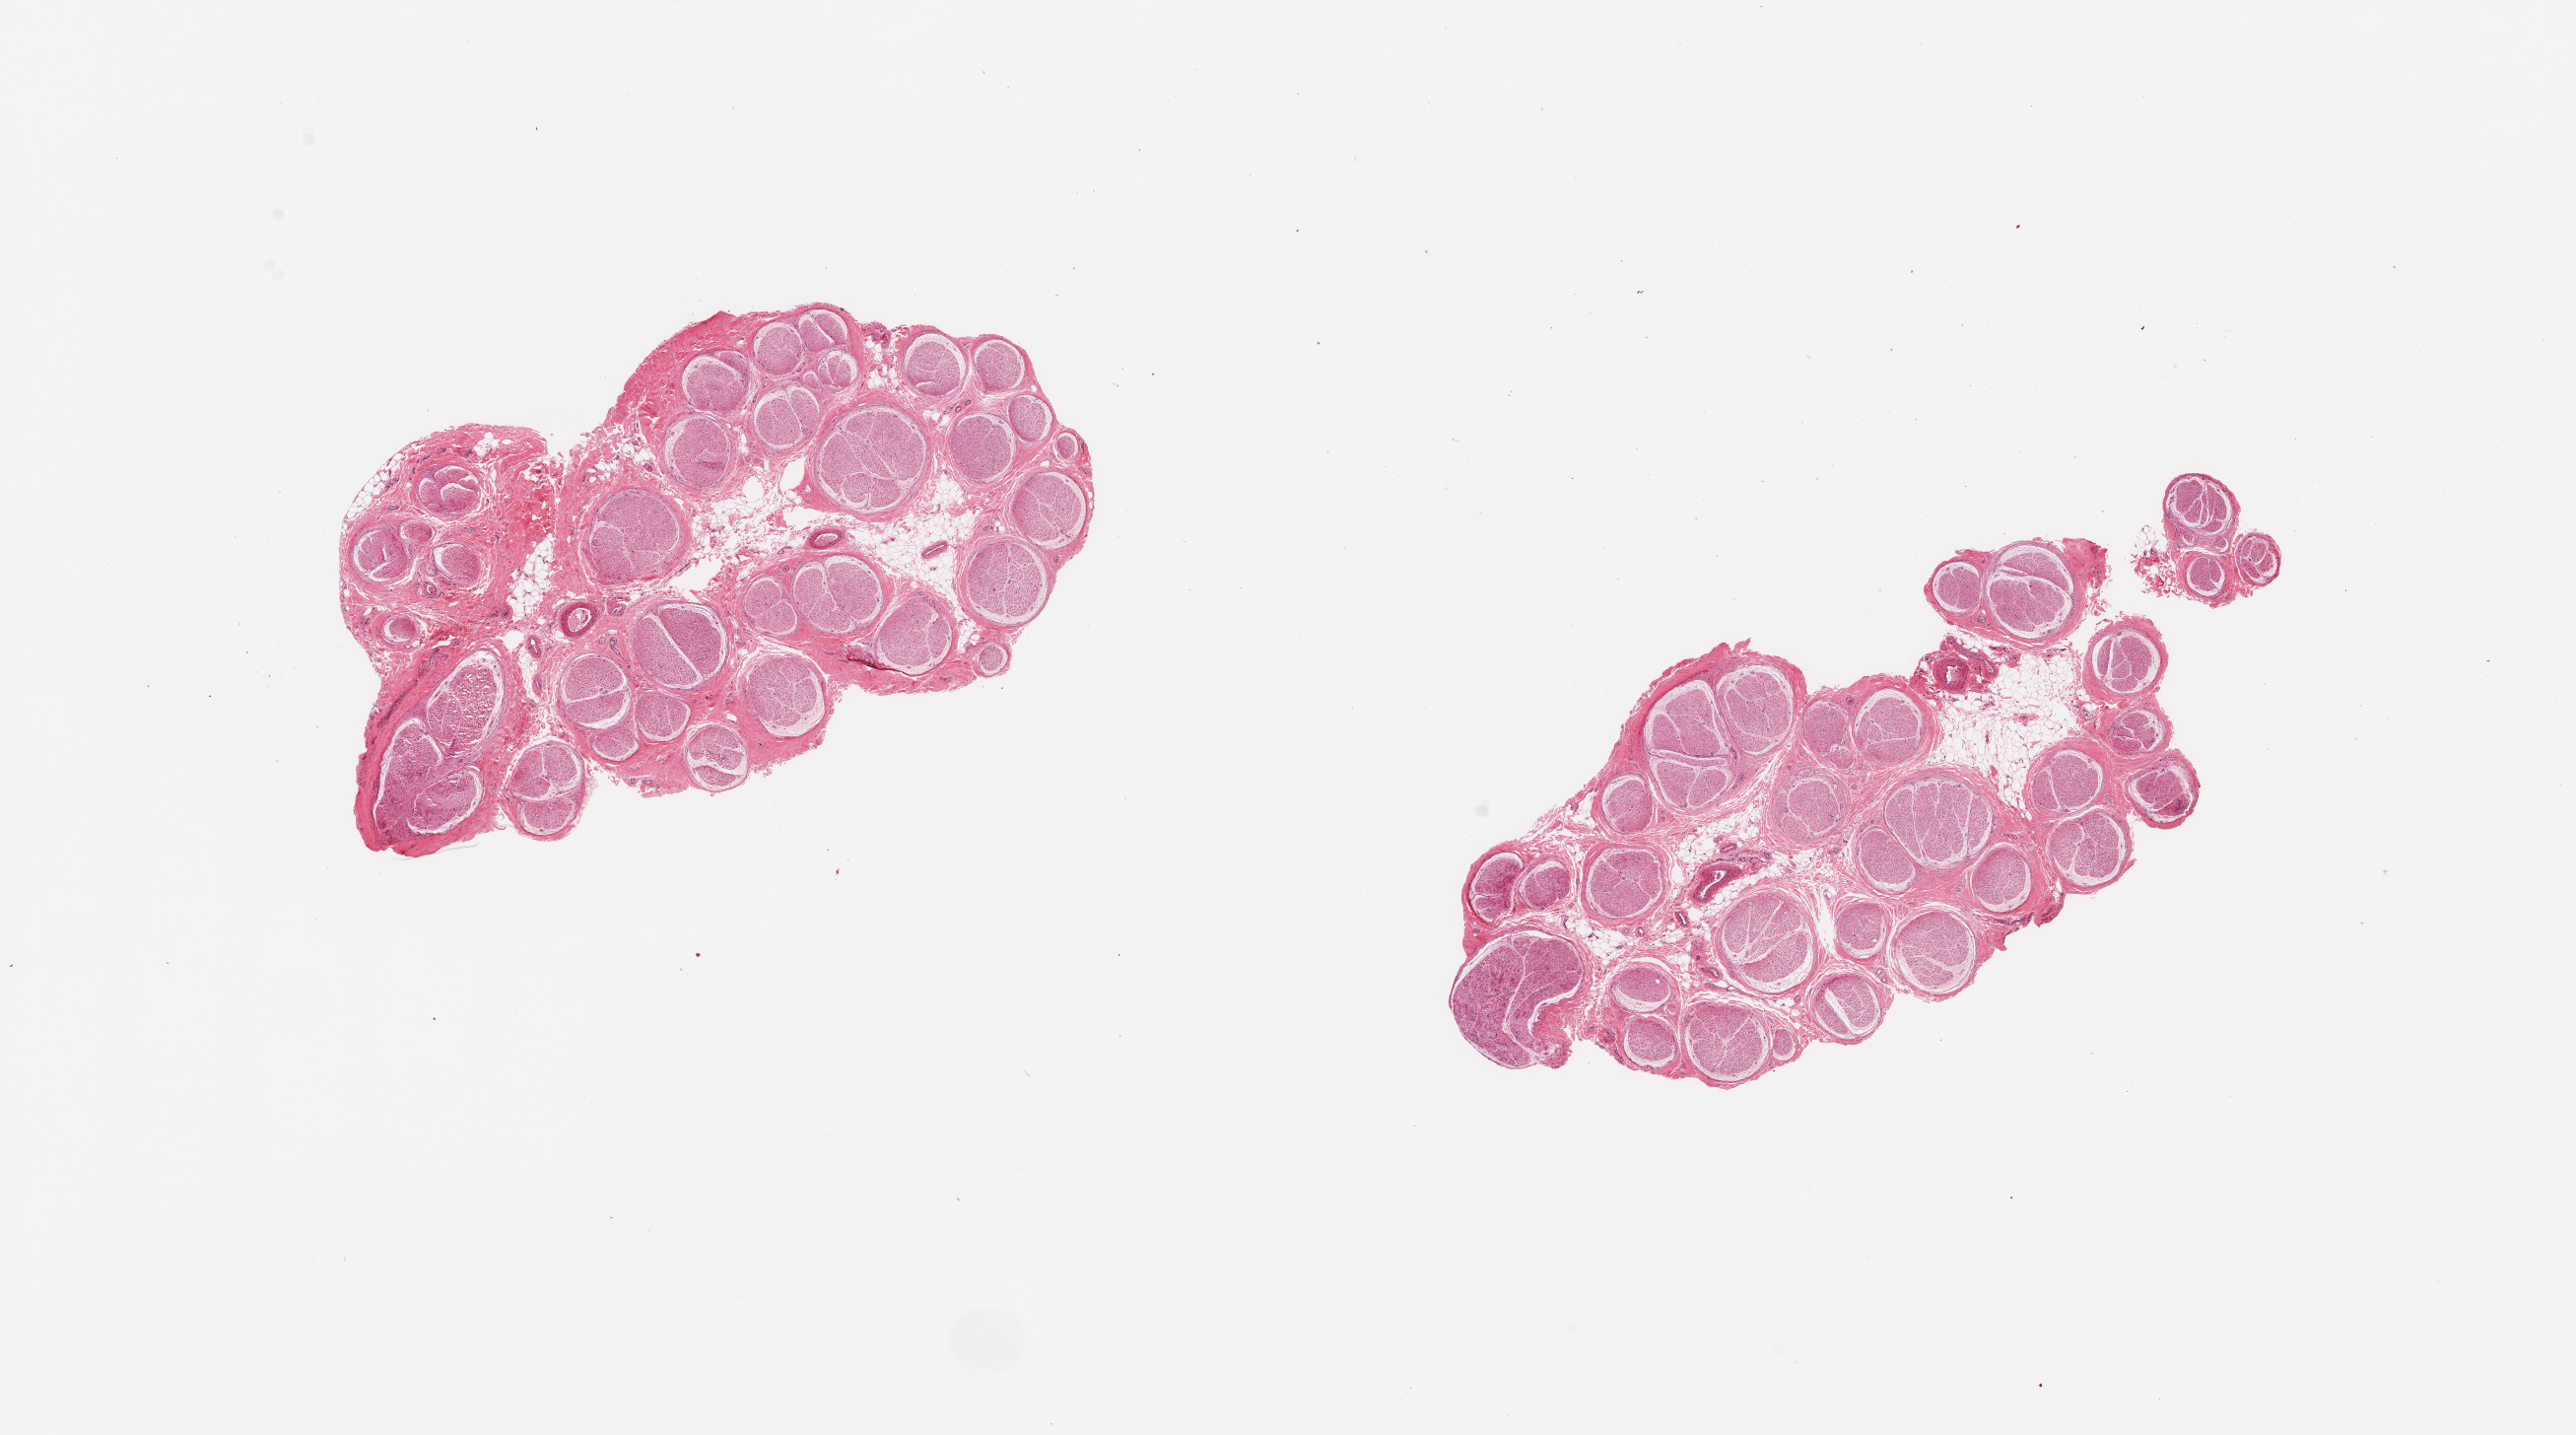
Hematoxylin and eosin (H&E) whole-slide image, brightfield — shown as a low-resolution overview of the whole scanned area (about 20.7 x 11.5 mm, from a 20x scan). PAXgene-fixed paraffin-embedded (PFPE) section. Section of tibial nerve (target tissue). Tissue donor sample. Male donor.
Review note (as recorded): 2 pieces, no adherant fat.